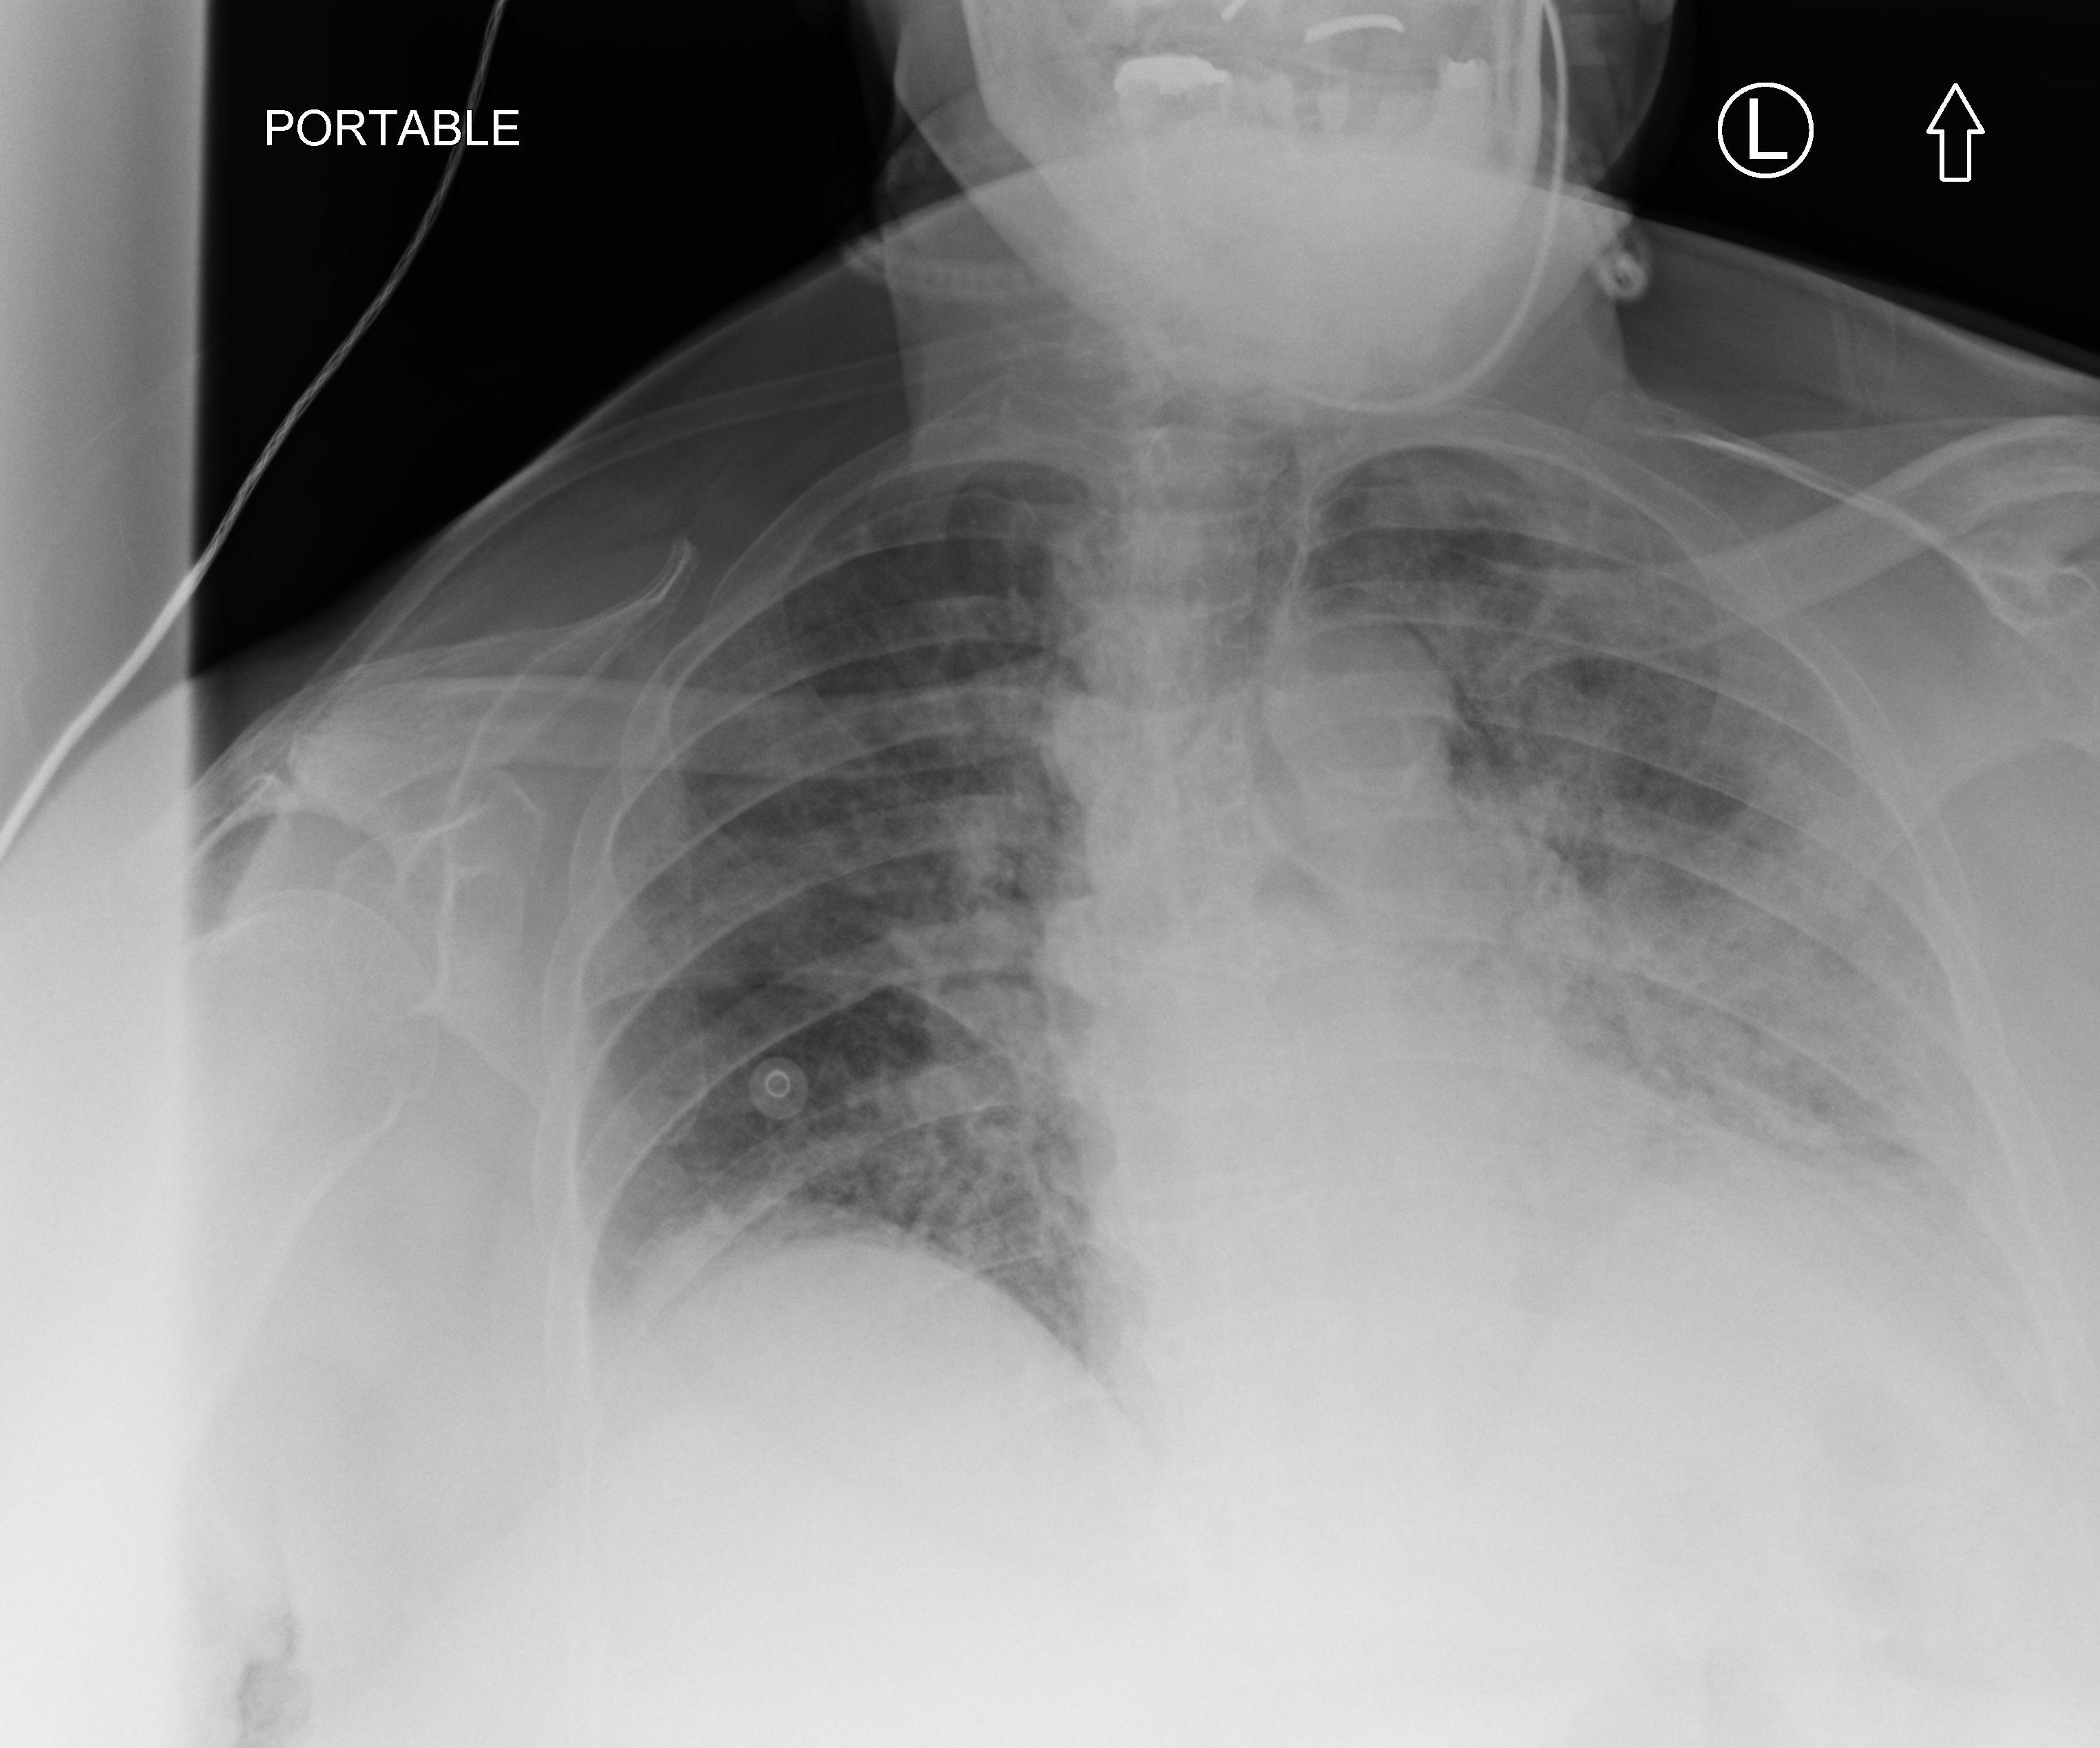
Portable chest radiograph; anteroposterior (AP) projection. Patient hospitalised with COVID-19; female, aged 75–90 years.
Hospital-stay facts (about this admission, not read from this image; timing relative to this image not recorded): mechanically ventilated during this hospital stay: no; admitted to intensive care during this hospital stay: no; chronic kidney disease (admission record): no.